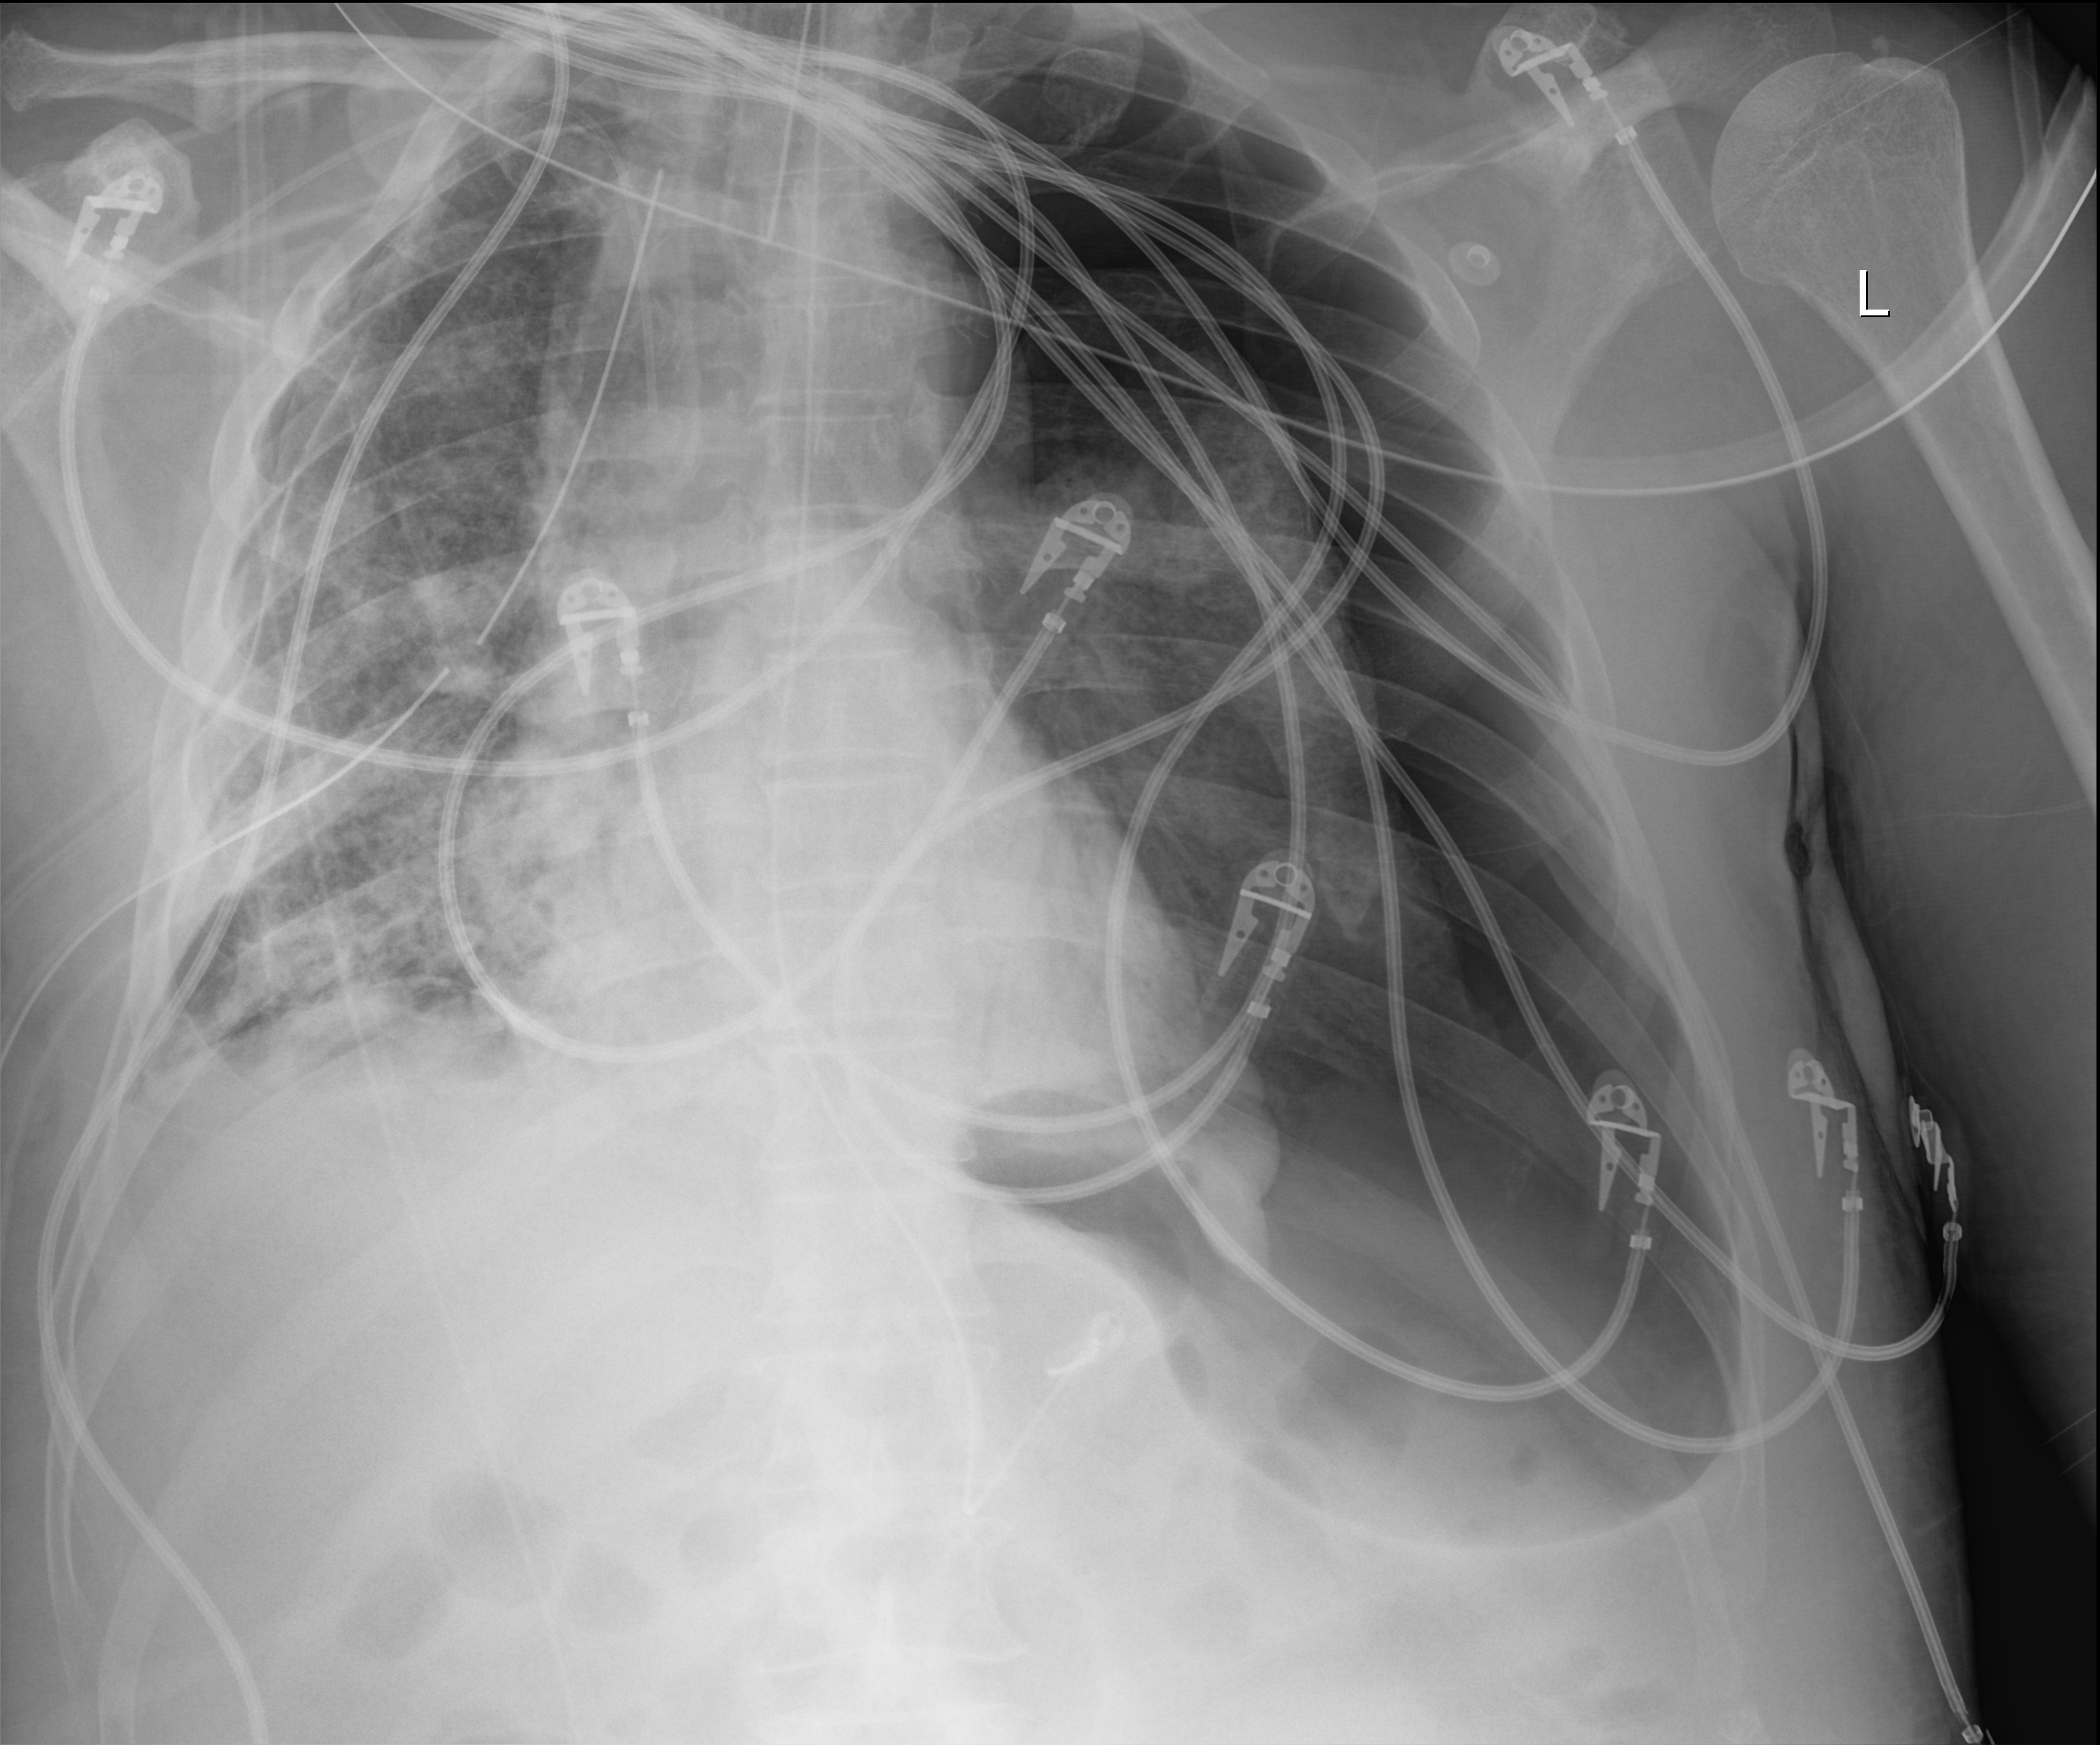
Bedside chest radiograph (digital radiography), anteroposterior (AP) projection. Patient hospitalised with COVID-19; male, aged 60–74 years.
Admission-level facts for this patient (not findings on this image; timing relative to this image not recorded): mechanically ventilated during this hospital stay: yes; smoking status (admission record): never.